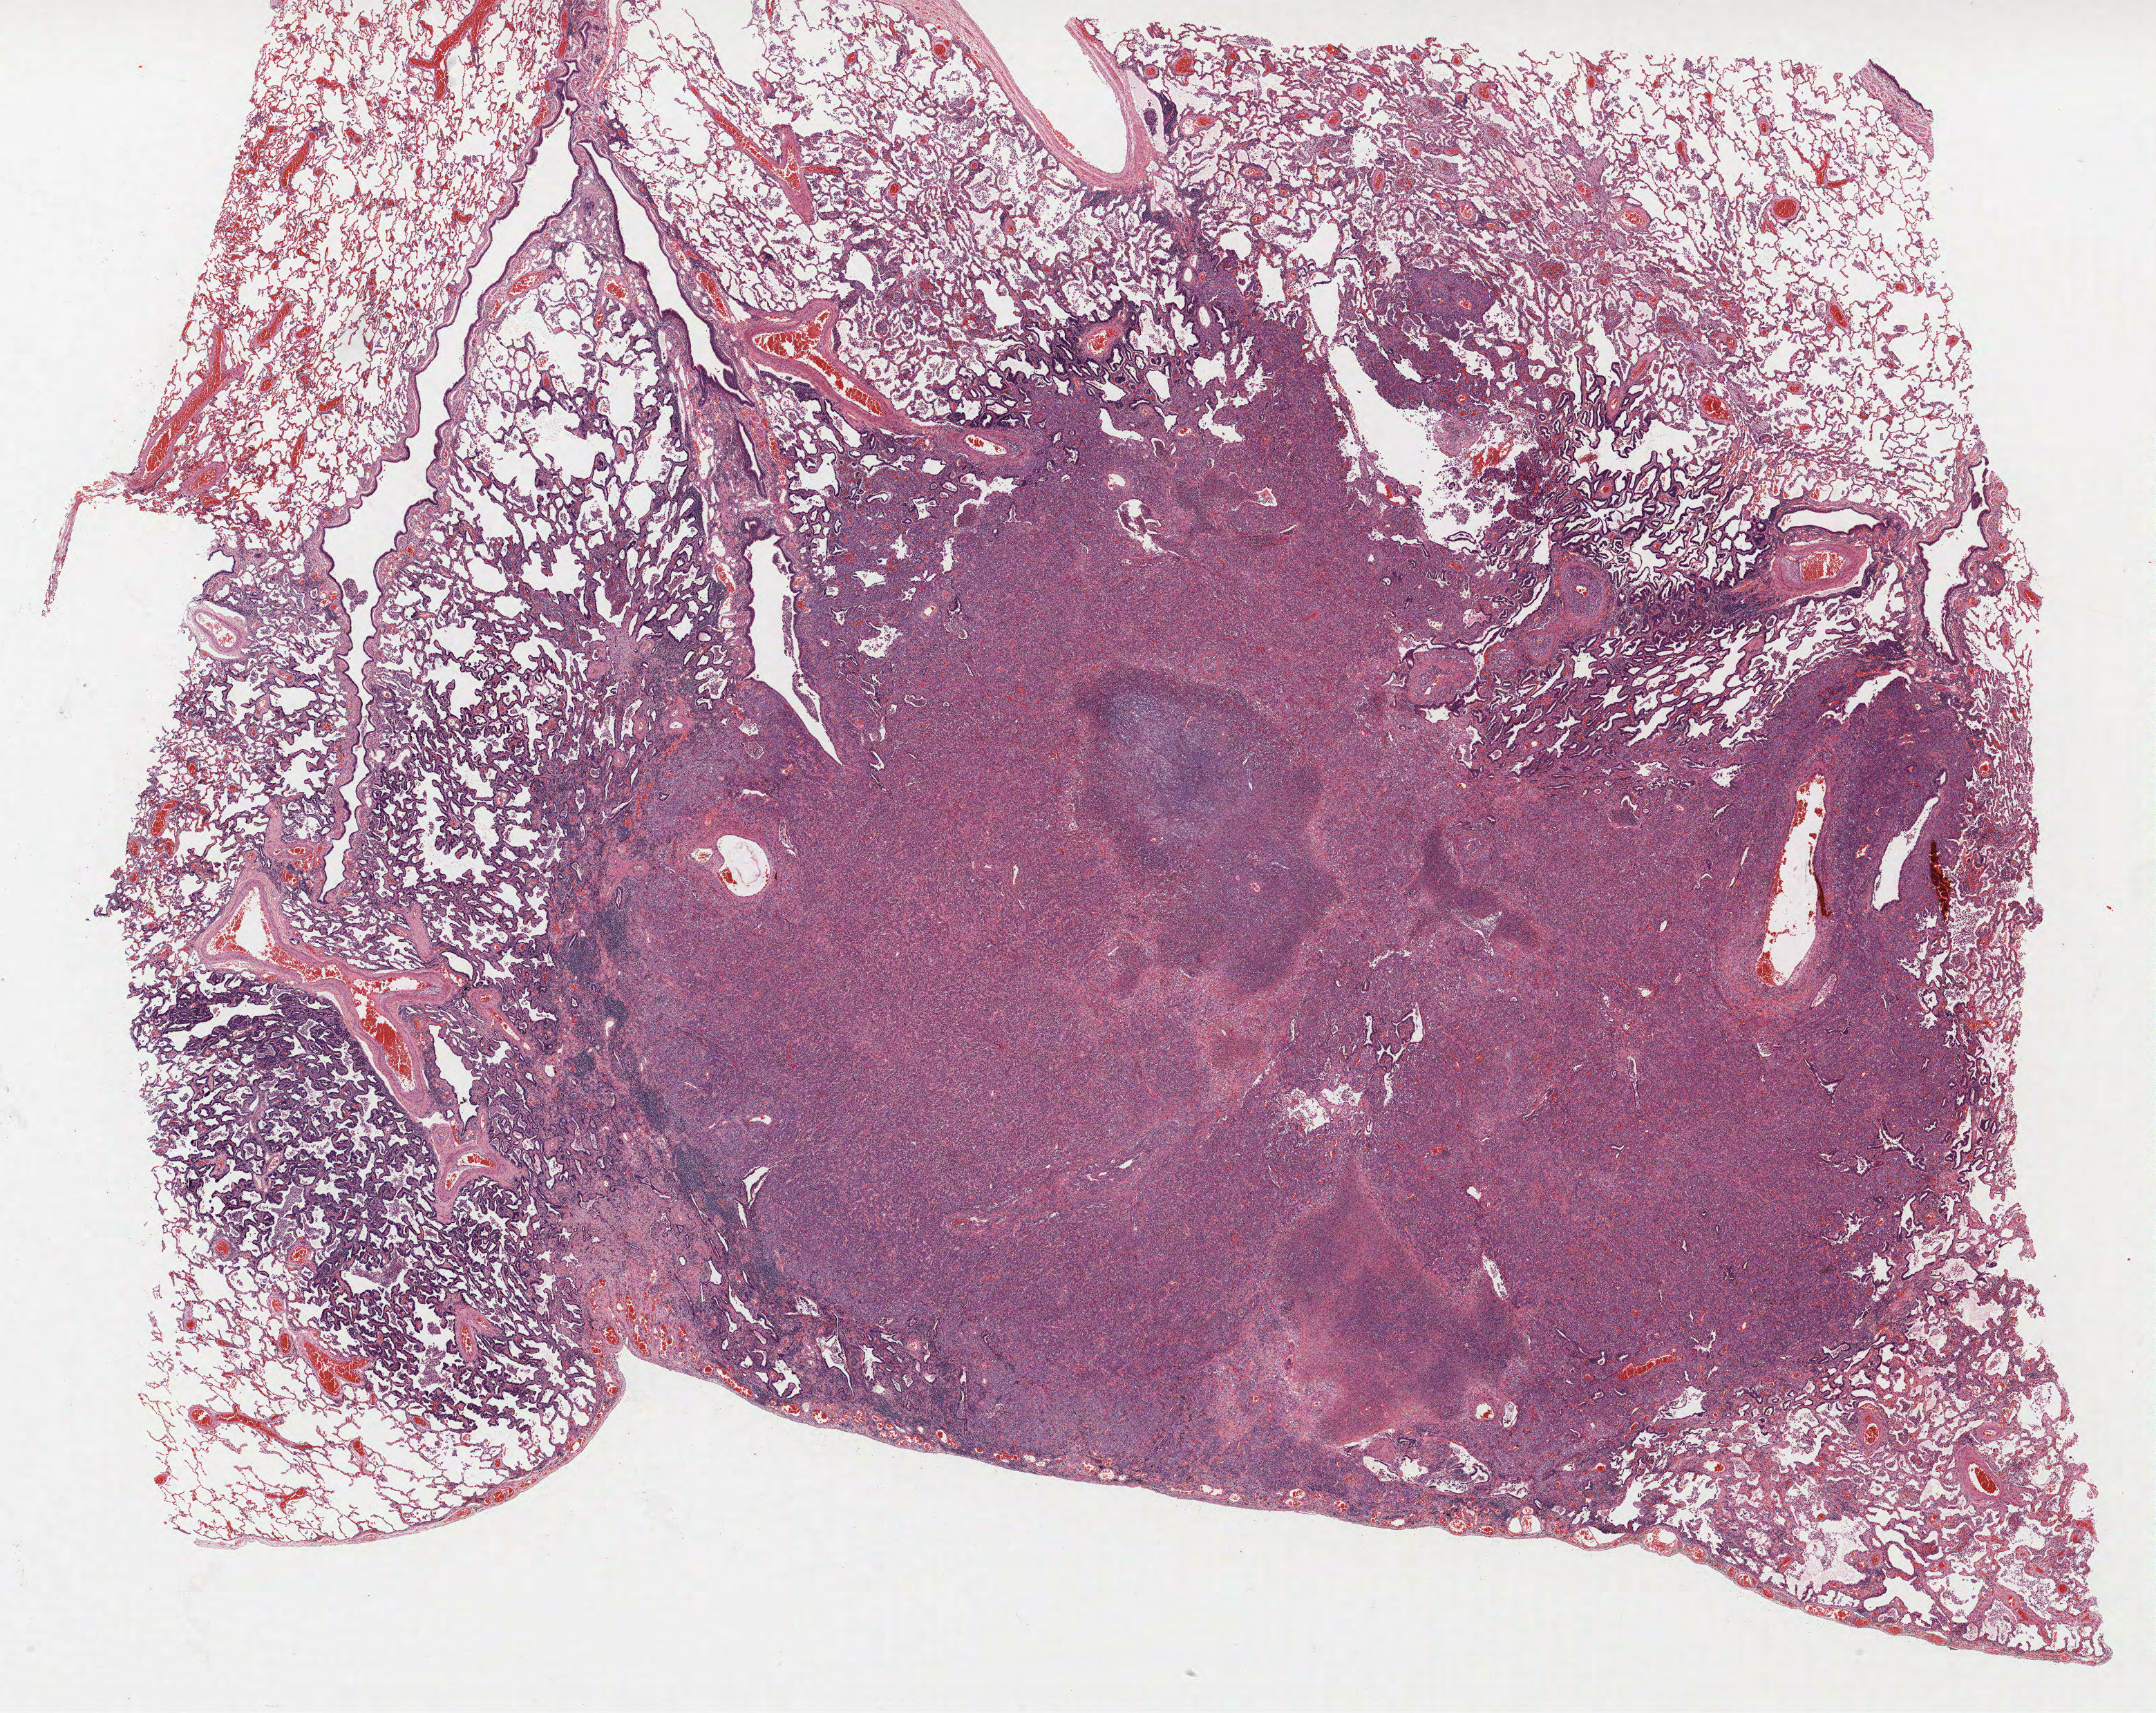
Whole-slide histology image, H&E-stained — low-resolution overview of the scanned area, about 25.0 x 19.8 mm (from a 40x scan). FFPE section. Lung tissue. Male patient, aged 60 at enrolment. Former smoker at enrolment. Grade: poorly differentiated (G3).
Participant's lung-cancer diagnosis: Adenocarcinoma, NOS (ICD-O-3 8140/3). Primary tumour location (clinical record): right lower lobe. Tumour size (pathology): 35 mm. Stage (AJCC 6th edition): IIB.